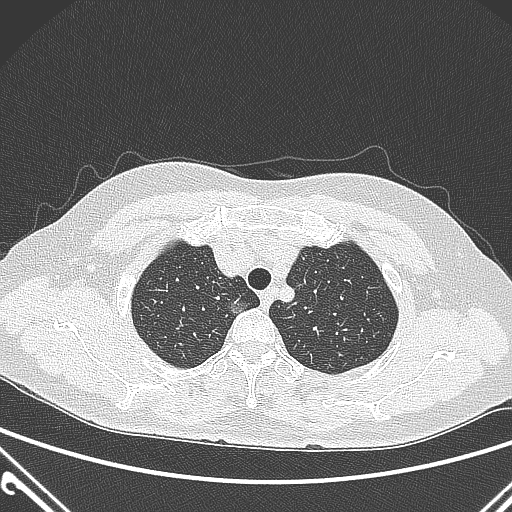
Chest CT, one axial slice; position 238 of 300 along the scan axis; 120 kVp; lung window (W 1500 / L -600 HU); 512 × 512 image matrix, field of view 350 × 350 mm. Female patient, age 54 years. Case-level facts recorded for this patient, not image findings: clinical TNM (as recorded): T1a N0 M0.
Annotated regions visible in this slice (rectangle marked by the reading radiologist):
- lung tumour (recorded histology: adenocarcinoma): bounding box <225,292,263,330> (left, top, right, bottom; pixels)